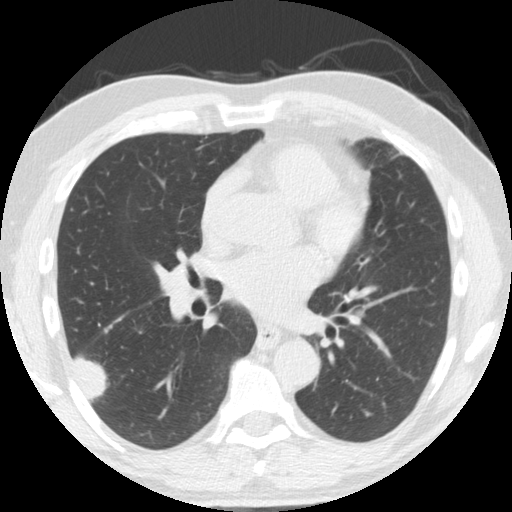
Axial slice from a low-dose chest CT screening exam. Second screening round (one year after baseline). Lung window (W 1500 / L -600 HU). 2.5 mm slice thickness. Standard (soft-tissue) reconstruction kernel (STANDARD). 120 kVp. Male participant, aged 61 years at enrolment. Former smoker at enrolment.
• Expert reader's lesion annotation, bounding box [x1, y1, x2, y2] px = [52, 328, 119, 402].
• The exam's reader record, not a measurement of the box and not confirmed to be the same lesion: non-calcified nodule or mass ≥4 mm, right lower lobe, 33 × 19 mm, smooth margins, soft tissue attenuation, pre-existing on the prior screen: yes; interval growth: yes.
• Later outcome: lung cancer diagnosed 30 days after this screen — adenosquamous carcinoma, right lower lobe, poorly differentiated (G3), stage IV (AJCC 6th edition), 45 mm at pathology.